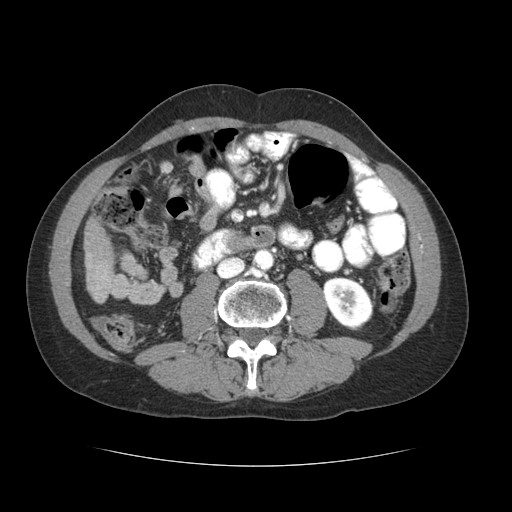
Contrast-enhanced abdominal CT (liver protocol), one axial slice. Slice 7 of 69 in the series (ordered by position). Reconstruction kernel STANDARD. 120 kVp. Soft-tissue window (W 400 / L 40 HU). 512 × 512 image matrix. Case-level facts recorded for this patient, not image findings: diagnosis: hepatocellular carcinoma (patient treated with transarterial chemoembolisation; whether this scan precedes or follows treatment is not stated here); TNM stage (as recorded): Stage-II; Child-Pugh class: B; tumour differentiation: poorly differentiated; tumour nodularity: multinodular.
Structures marked on this image (semi-automatic segmentation, software-assisted and operator-edited):
- liver parenchyma outside the tumour (the mass and vessels are separate outlines, so this box may not span the whole liver): bounding box <84,218,114,295> (left, top, right, bottom; pixels)
- liver vessels: <97,275,106,289>